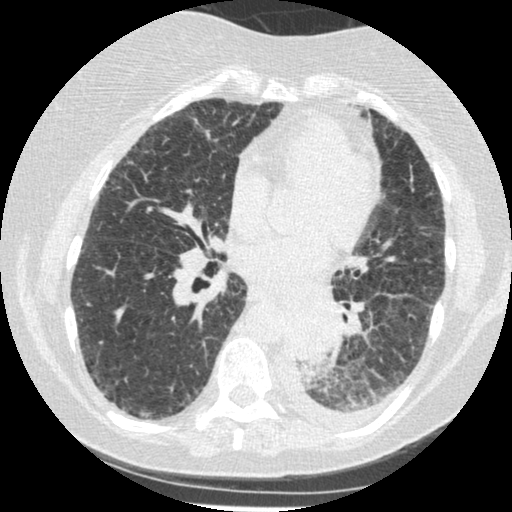
Axial slice from a low-dose chest CT screening exam, third annual screen, lung window (W 1500 / L -600 HU), slice 236 of 341 in the series, 512 × 512 image matrix, field of view 310 × 310 mm. Female, age 60 years at enrolment. Former smoker at enrolment.
- Expert-annotated lung lesion, bounding box [x1, y1, x2, y2] px = [276, 303, 343, 375].
- Reader record for this screening exam (exam-level; its link to the box is not recorded): non-calcified nodule or mass ≥4 mm, left lower lobe, 54 × 38 mm, smooth margins, soft tissue attenuation, pre-existing on the prior screen: yes; interval growth: yes.
- Official screen result: positive, other.